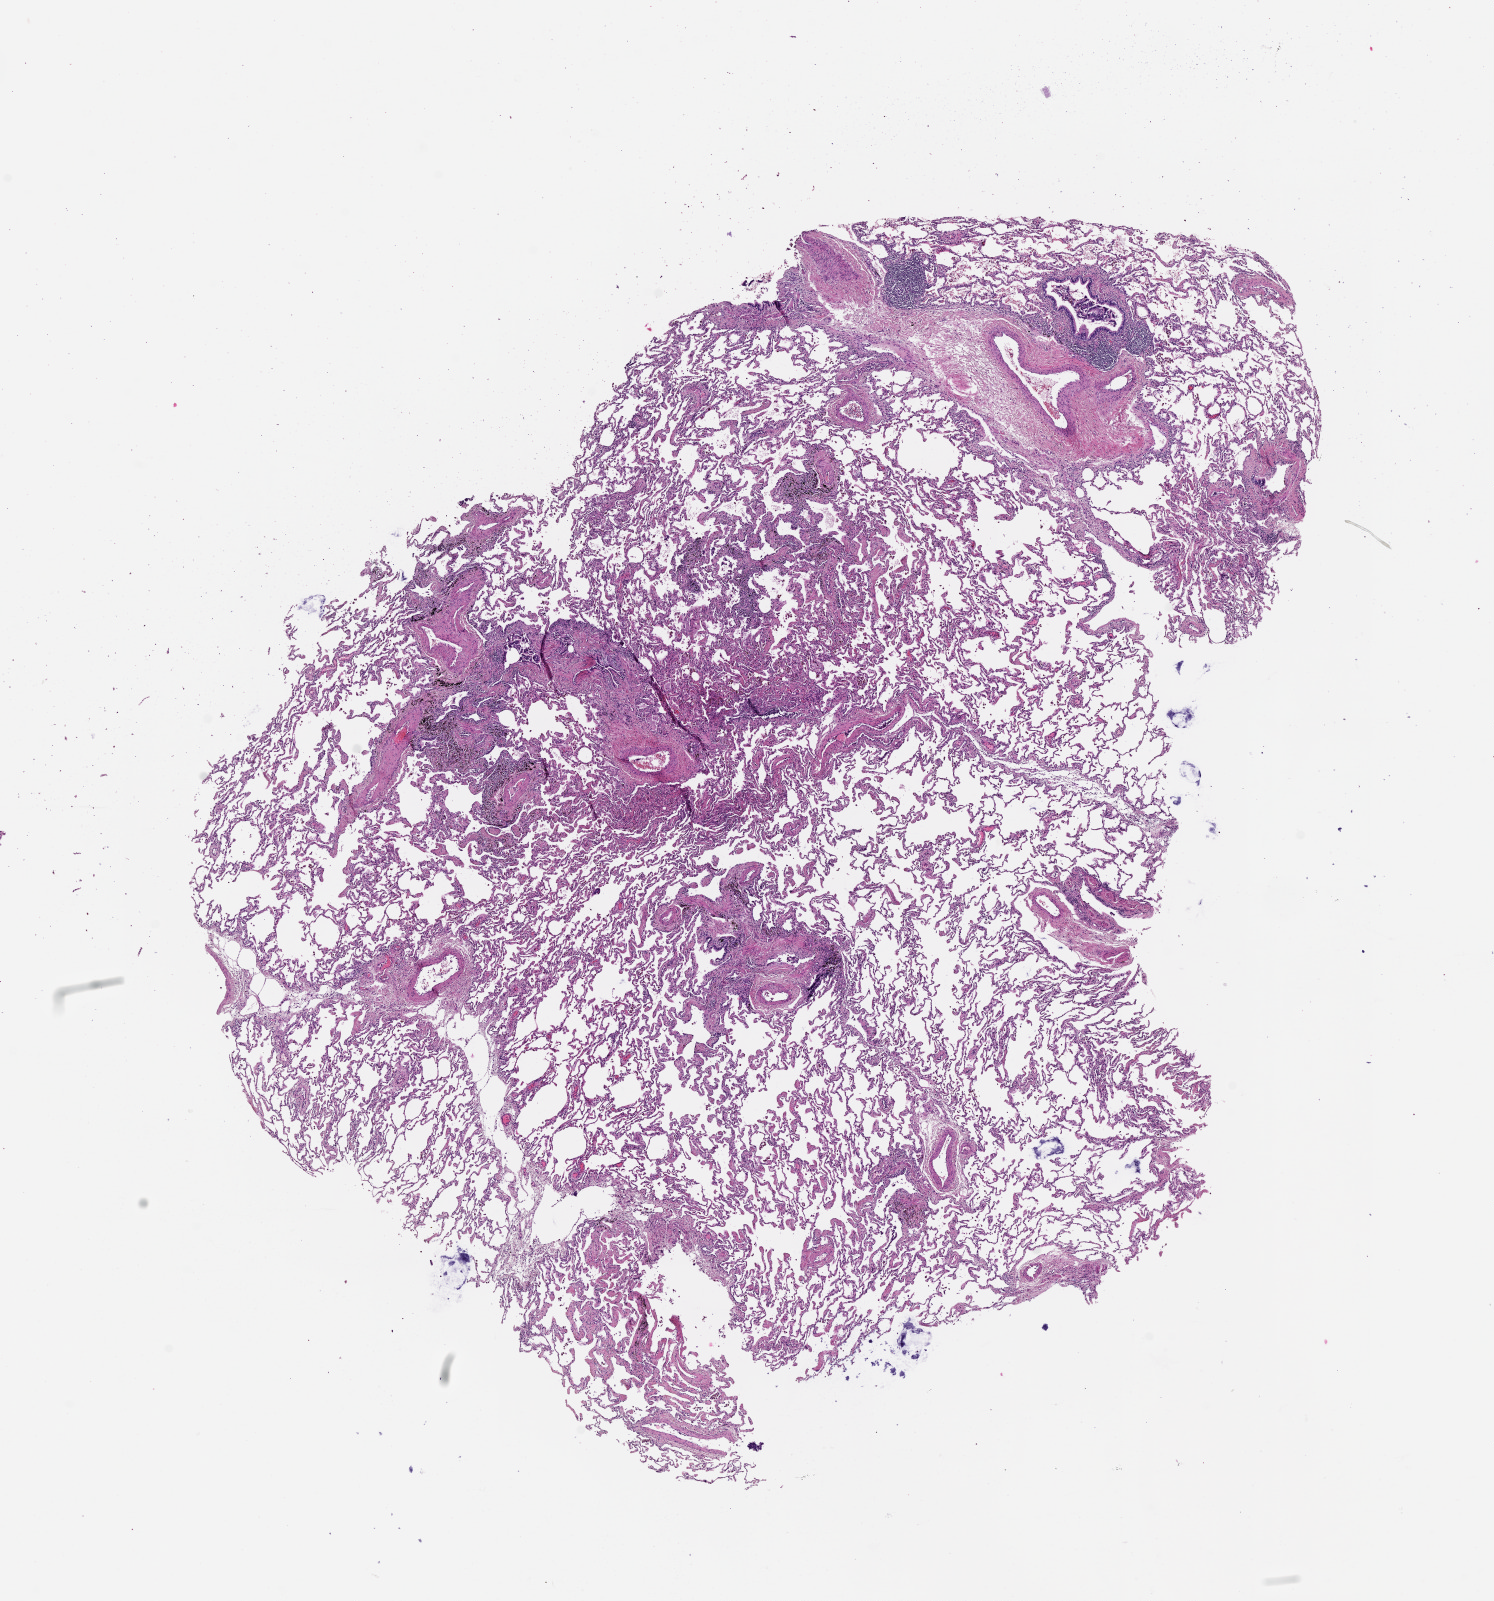
Digitized Hematoxylin and eosin (H&E) stained tissue section (whole slide), low-resolution overview of the scanned area, about 12.0 x 12.9 mm (acquisition: 20x scan); lung, tissue type not recorded.
Patient diagnosis (cohort enrolment): squamous cell carcinoma (lung).